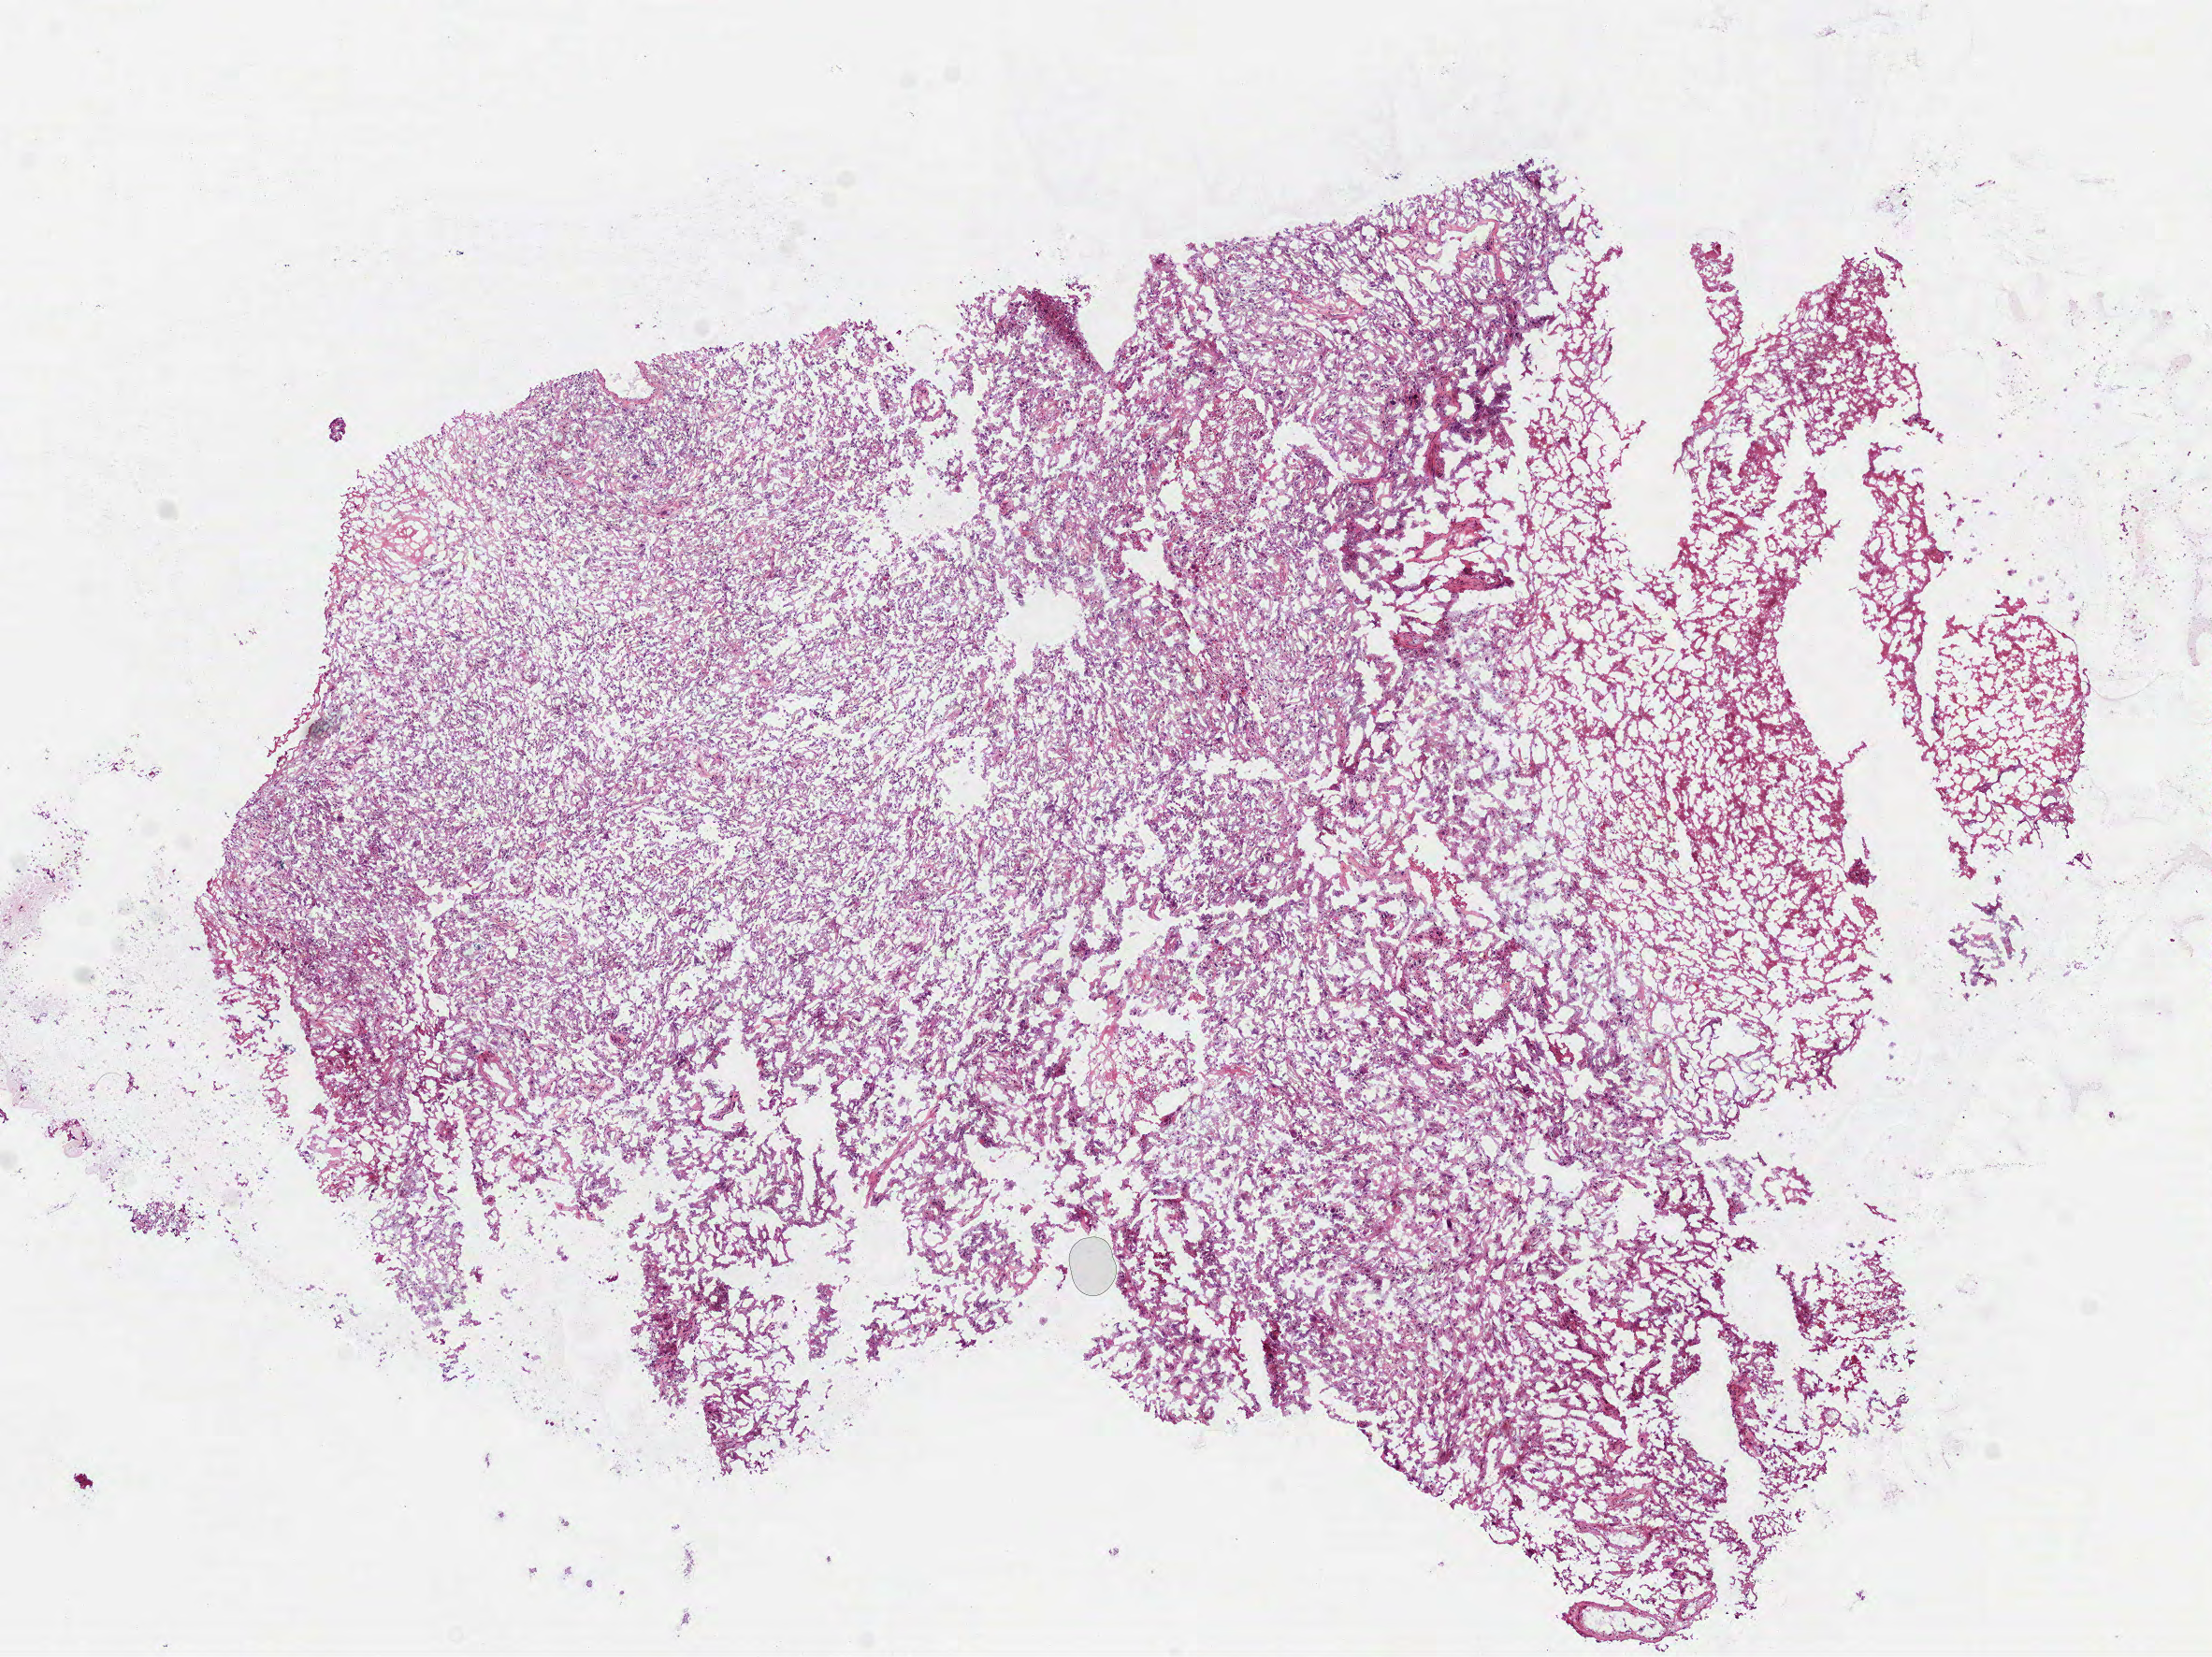
Whole-slide histology image, H&E-stained, a low-resolution overview of the entire scanned area, about 9.5 x 7.1 mm (acquisition: 40x scan); frozen section; sample: recurrent tumour, brain. Male, age 51 years at initial diagnosis. Pathologist review of this section (percent, as recorded): tumour cells 90%, tumour nuclei 65%, normal cells 0%, stromal cells 0%, necrosis 10%.
• this section: recurrent tumour
• patient diagnosis: Glioblastoma